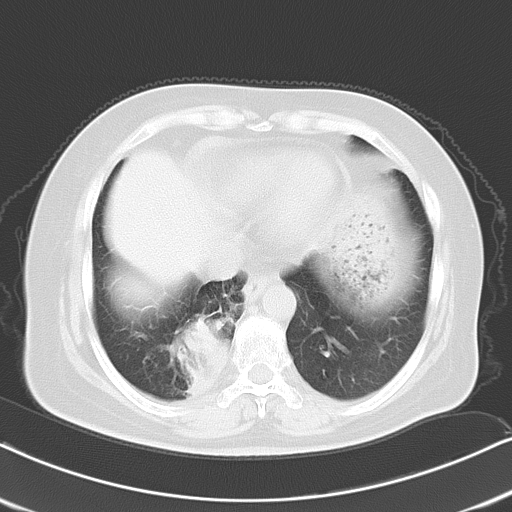
Chest CT, one axial slice. Slice 5 of 21 in the series (ordered by position). Lung window (W 1500 / L -600 HU). 512 × 512 image matrix, field of view 326 × 326 mm. Patient: female, 61 years. Case-level facts recorded for this patient, not image findings: clinical TNM (as recorded): T1b N0 M1b.
Annotated regions visible in this slice (bounding box drawn by a radiologist):
- lung tumour (recorded histology: squamous cell carcinoma): bounding box <167,314,228,400> (left, top, right, bottom; pixels)